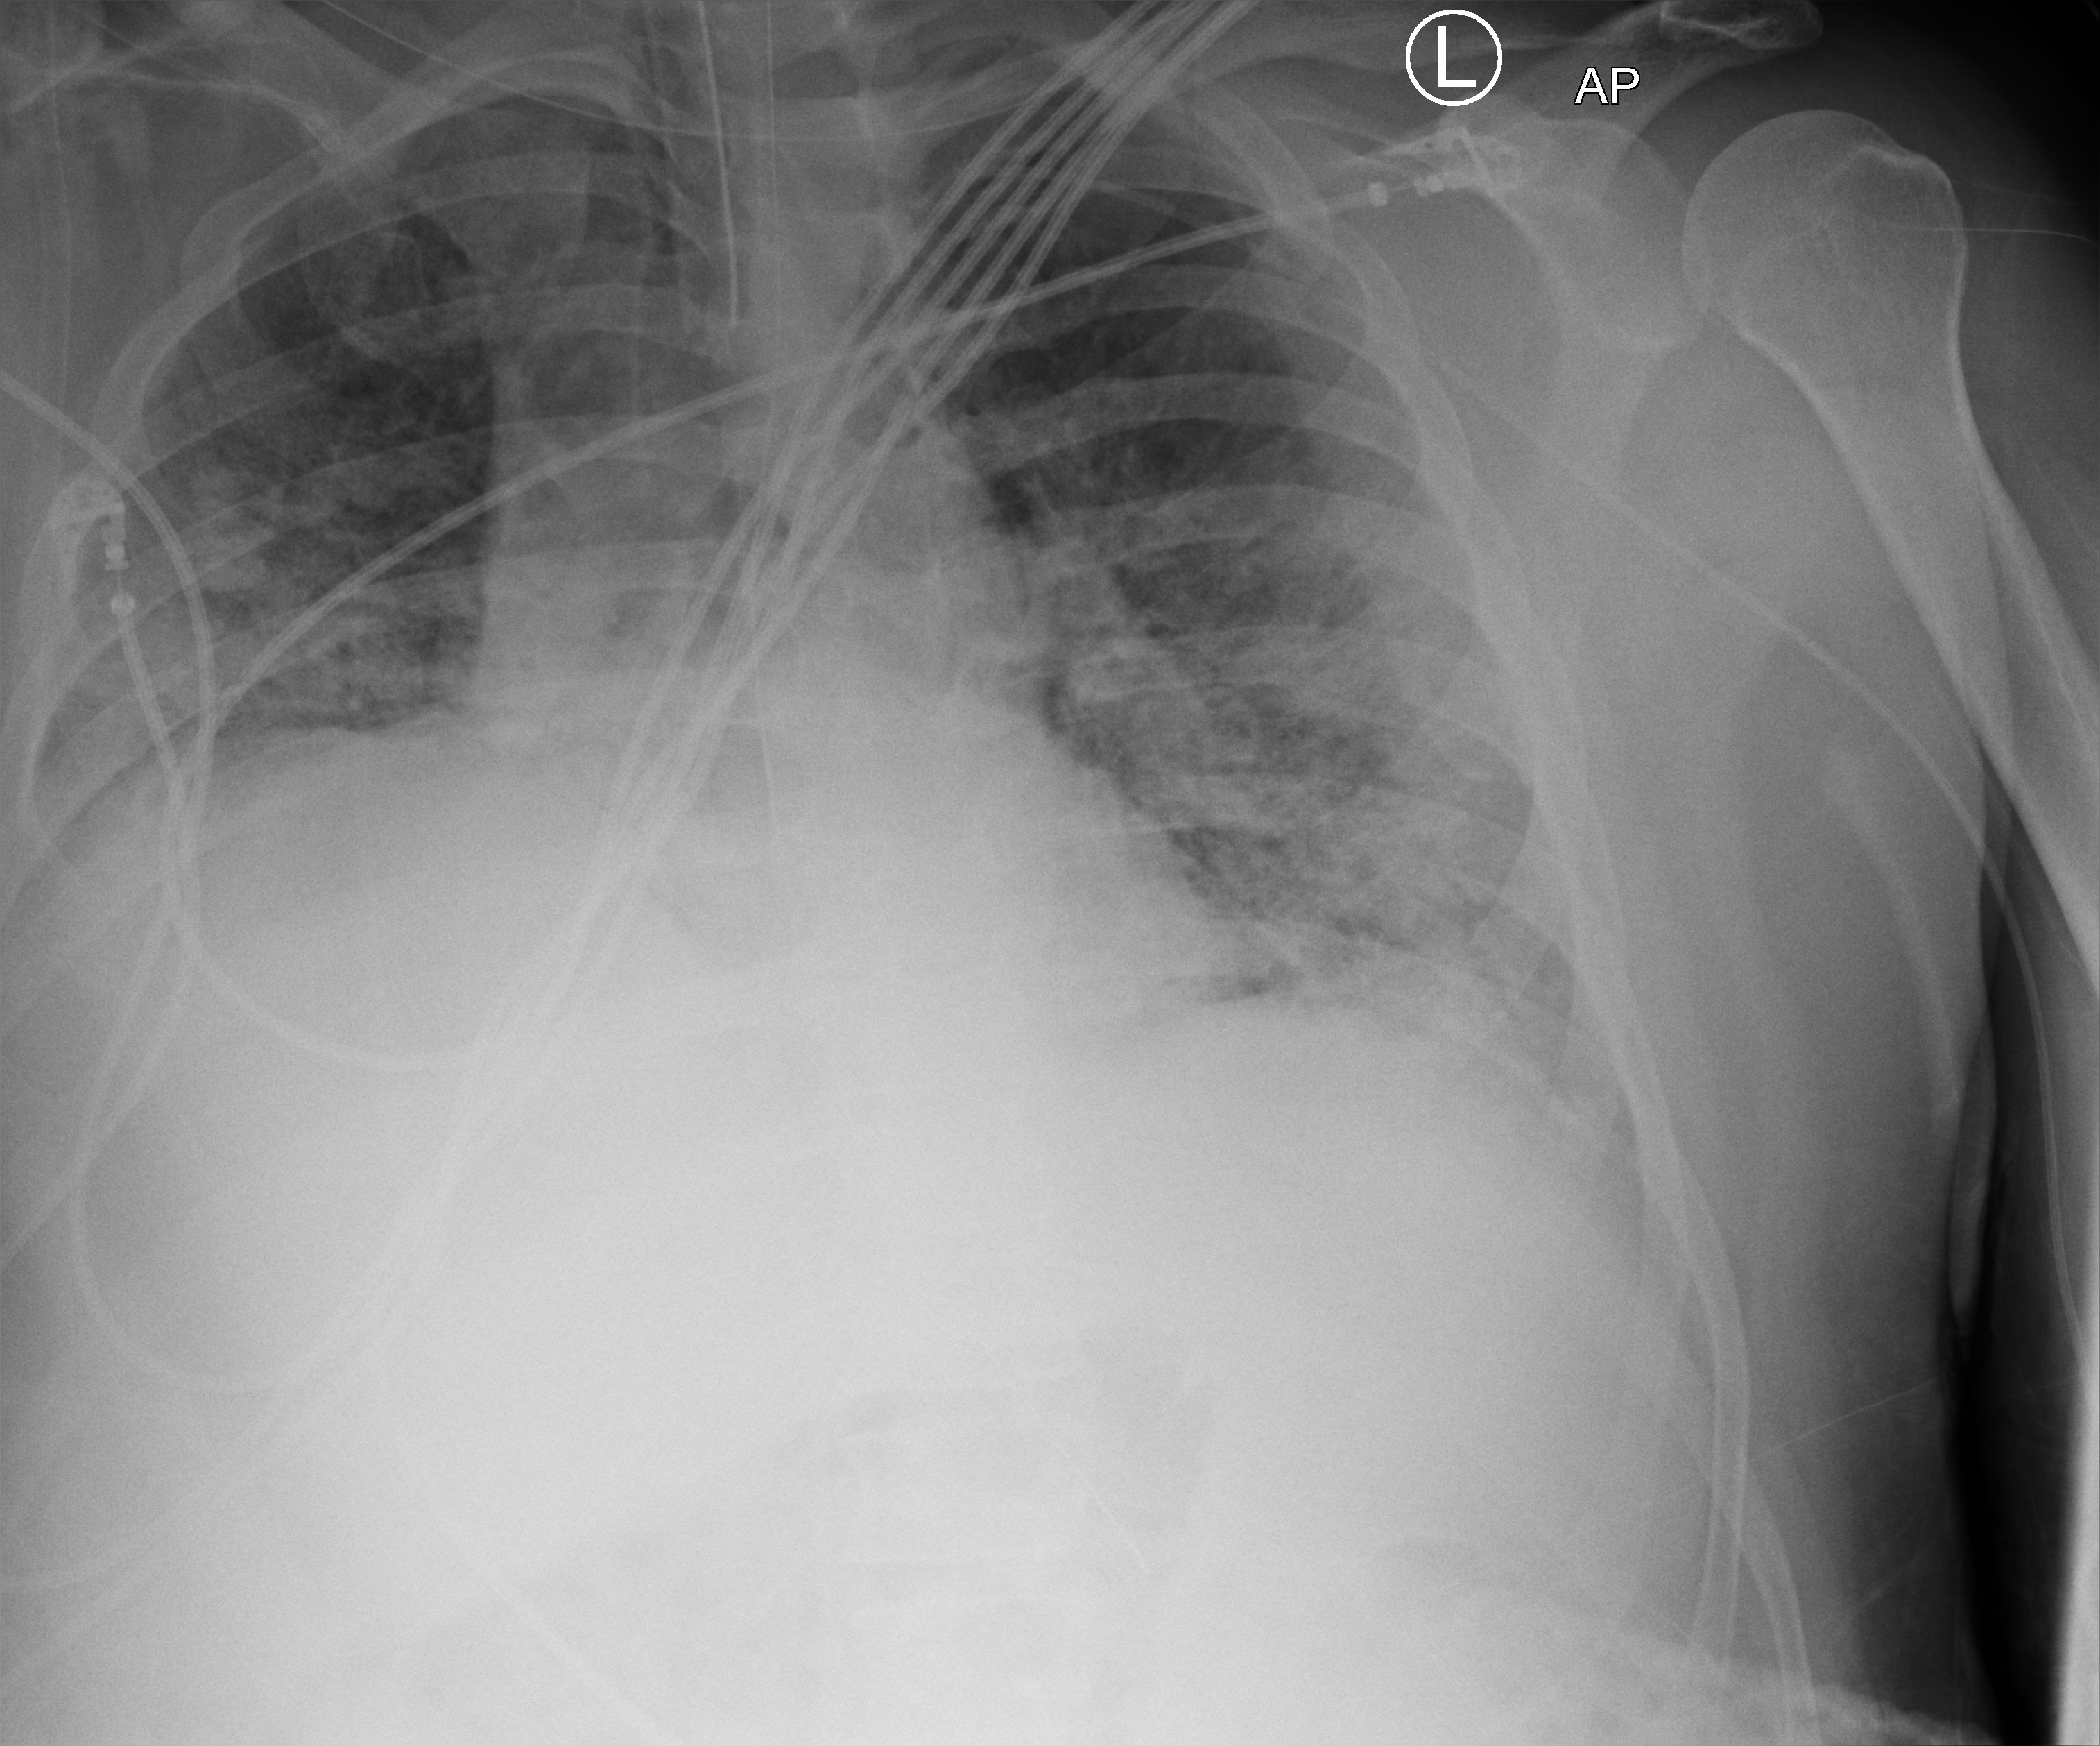
Bedside chest radiograph (computed radiography), anteroposterior (AP) projection. Male patient hospitalised with COVID-19, age 18–59 years.
Hospital-stay facts (about this admission, not read from this image; timing relative to this image not recorded): other chronic lung disease (admission record): no.